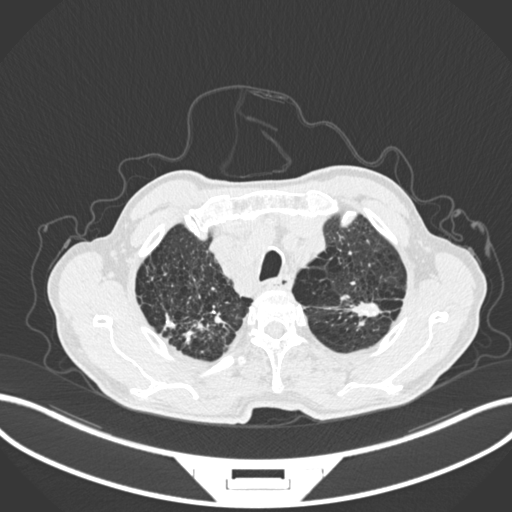
Chest CT, one axial slice; 120 kVp; lung window (W 1500 / L -600 HU); 1 mm slice thickness; 512 × 512 image matrix. Patient: male, 74 years. Case-level facts recorded for this patient, not image findings: clinical TNM (as recorded): T2a N1 M0.
Structures marked on this image (bounding box drawn by a radiologist):
- lung tumour (recorded histology: adenocarcinoma): bounding box (x1, y1, x2, y2) in pixels: (345, 299, 384, 322)